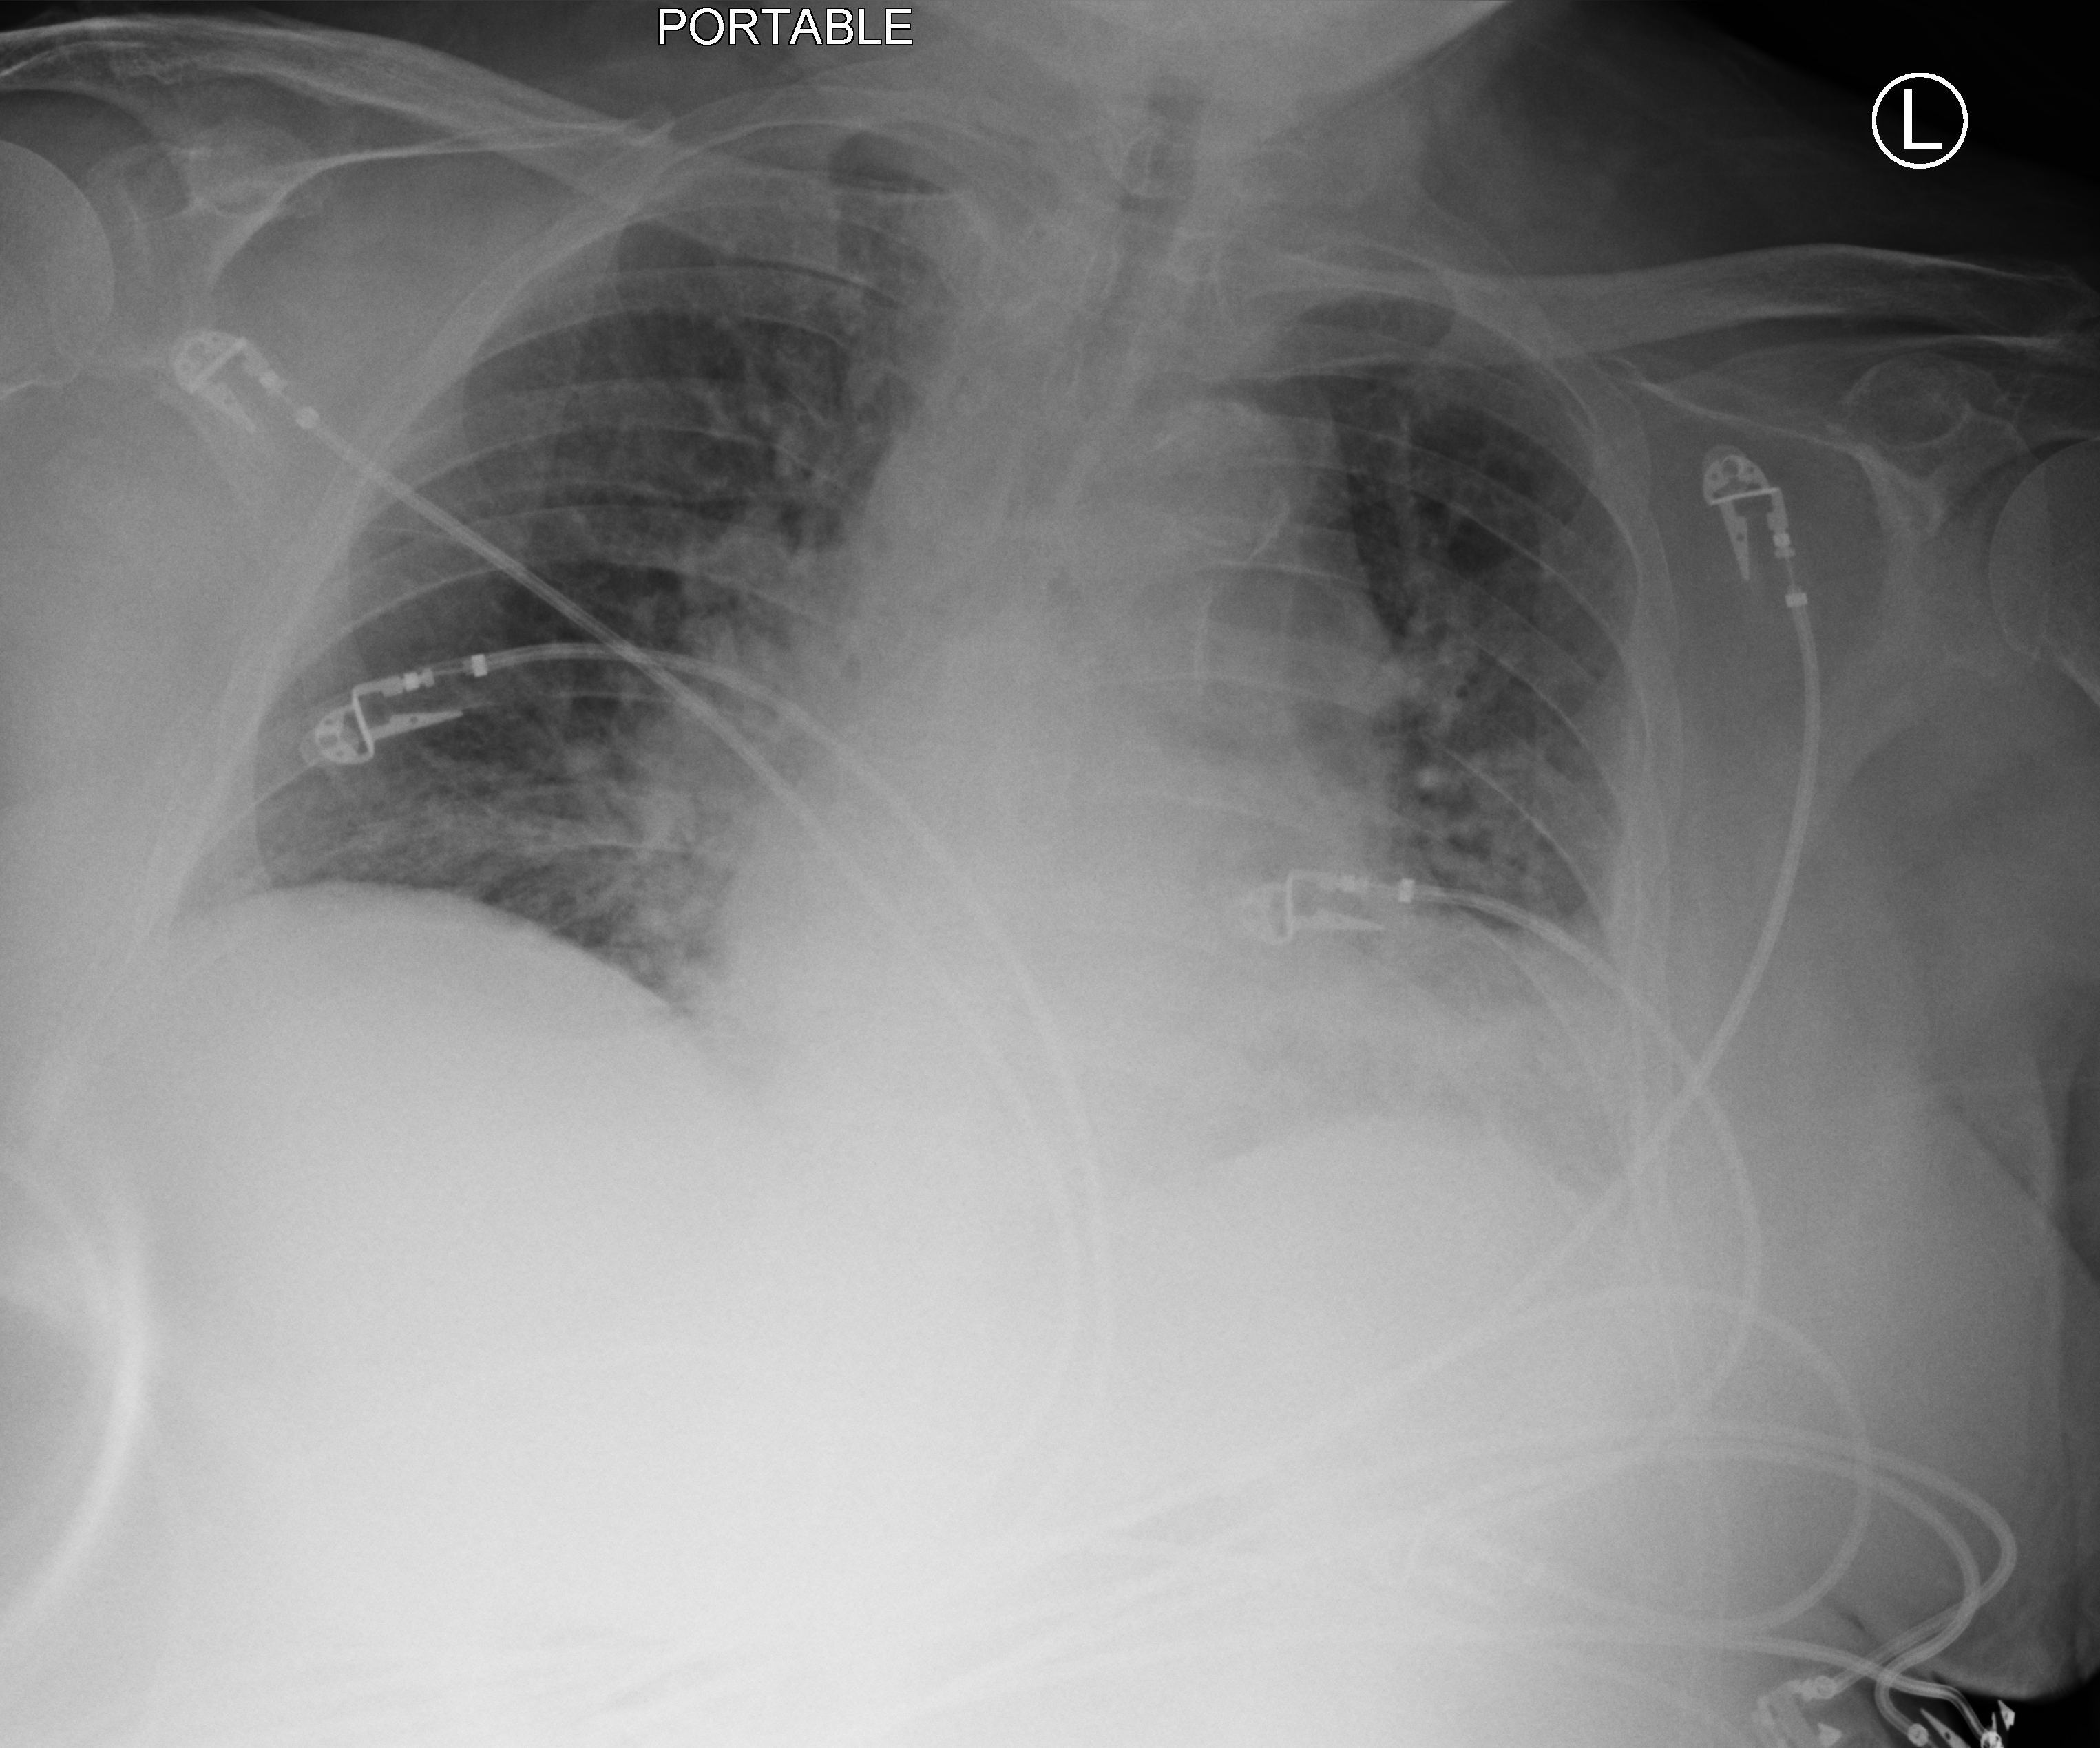
Portable chest radiograph. Patient hospitalised with COVID-19; male, aged 75–90 years.
Hospital-stay facts (about this admission, not read from this image; timing relative to this image not recorded): hypertension (admission record): no; smoking status (admission record): never; admitted to intensive care during this hospital stay: no.